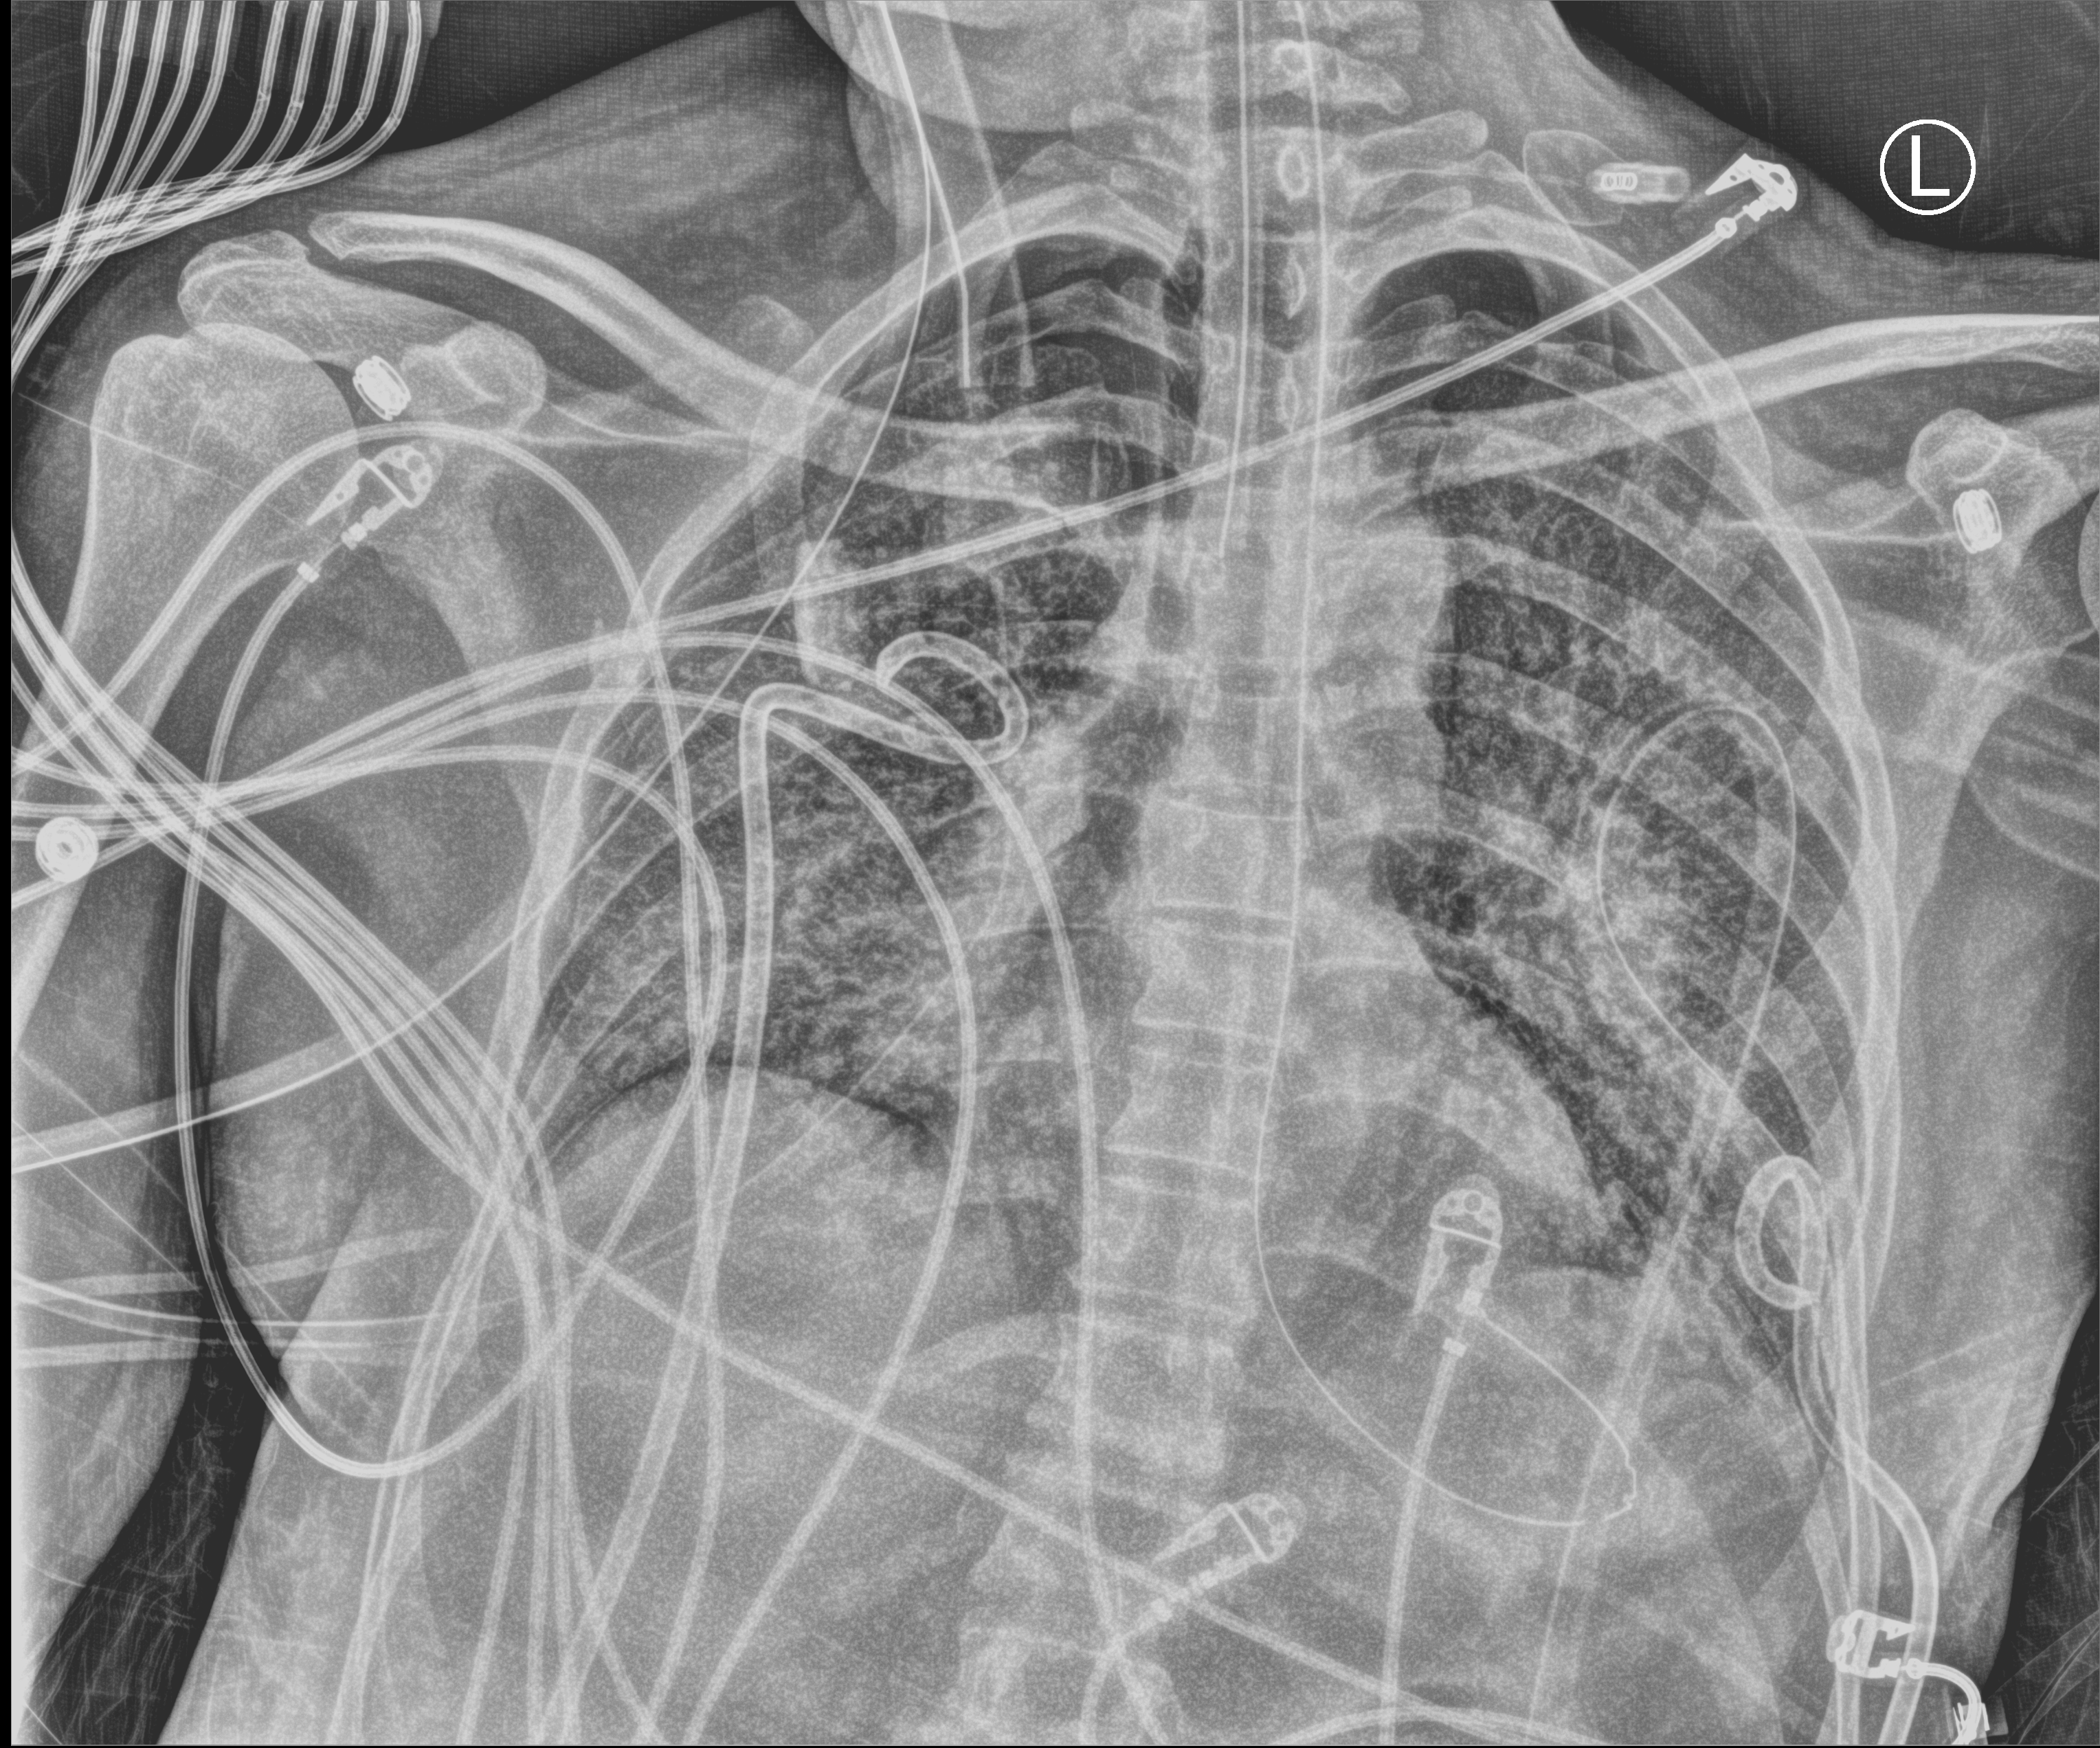
Bedside chest radiograph (computed radiography); anteroposterior (AP) projection. Patient hospitalised with COVID-19, aged 18–59 years.
Hospital-stay facts (about this admission, not read from this image; timing relative to this image not recorded): admitted to intensive care during this hospital stay: yes; diabetes (admission record): no; smoking status (admission record): never.